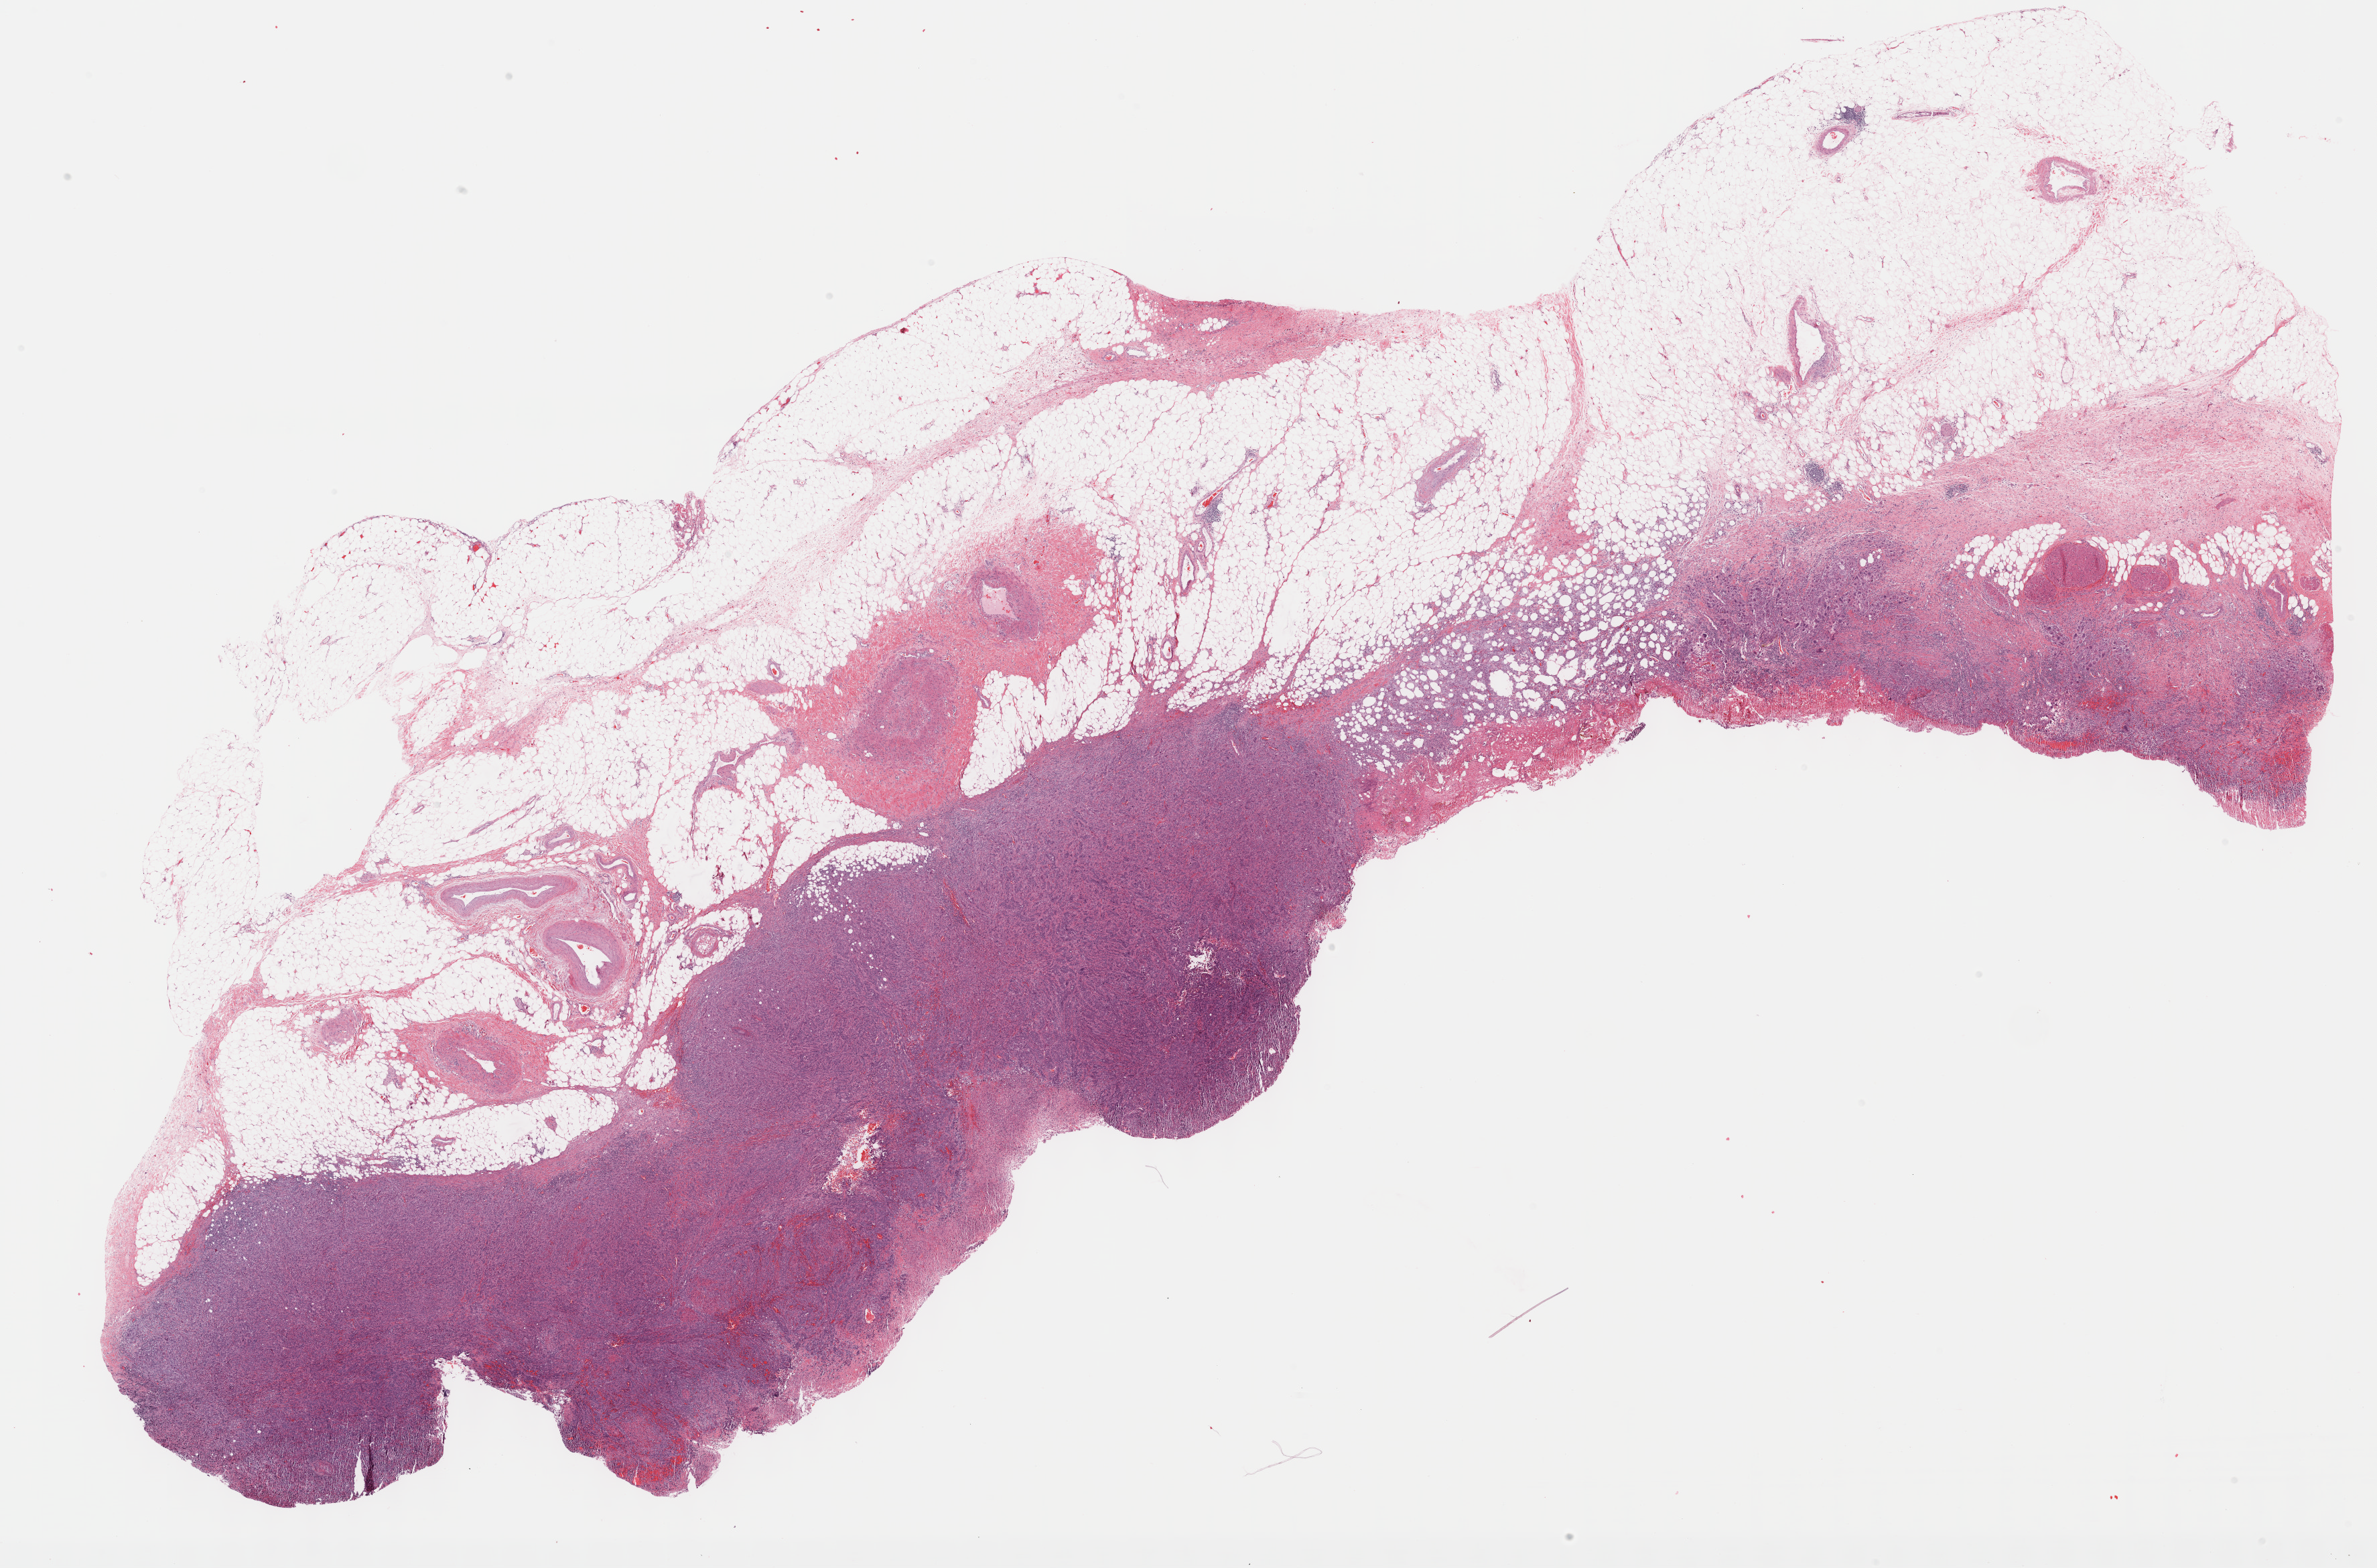
Digitized Hematoxylin and eosin (H&E) stained tissue section (whole slide), a low-resolution overview of the entire scanned area, about 28.7 x 18.9 mm (acquisition: 40x scan). Formalin-fixed paraffin-embedded (FFPE) diagnostic section. Sample: primary tumour, bladder. Male patient. Histologic grade: high grade.
* TNM: T3b N0 M0
* histologic diagnosis: Papillary transitional cell carcinoma
* AJCC pathologic stage: III (6th edition)